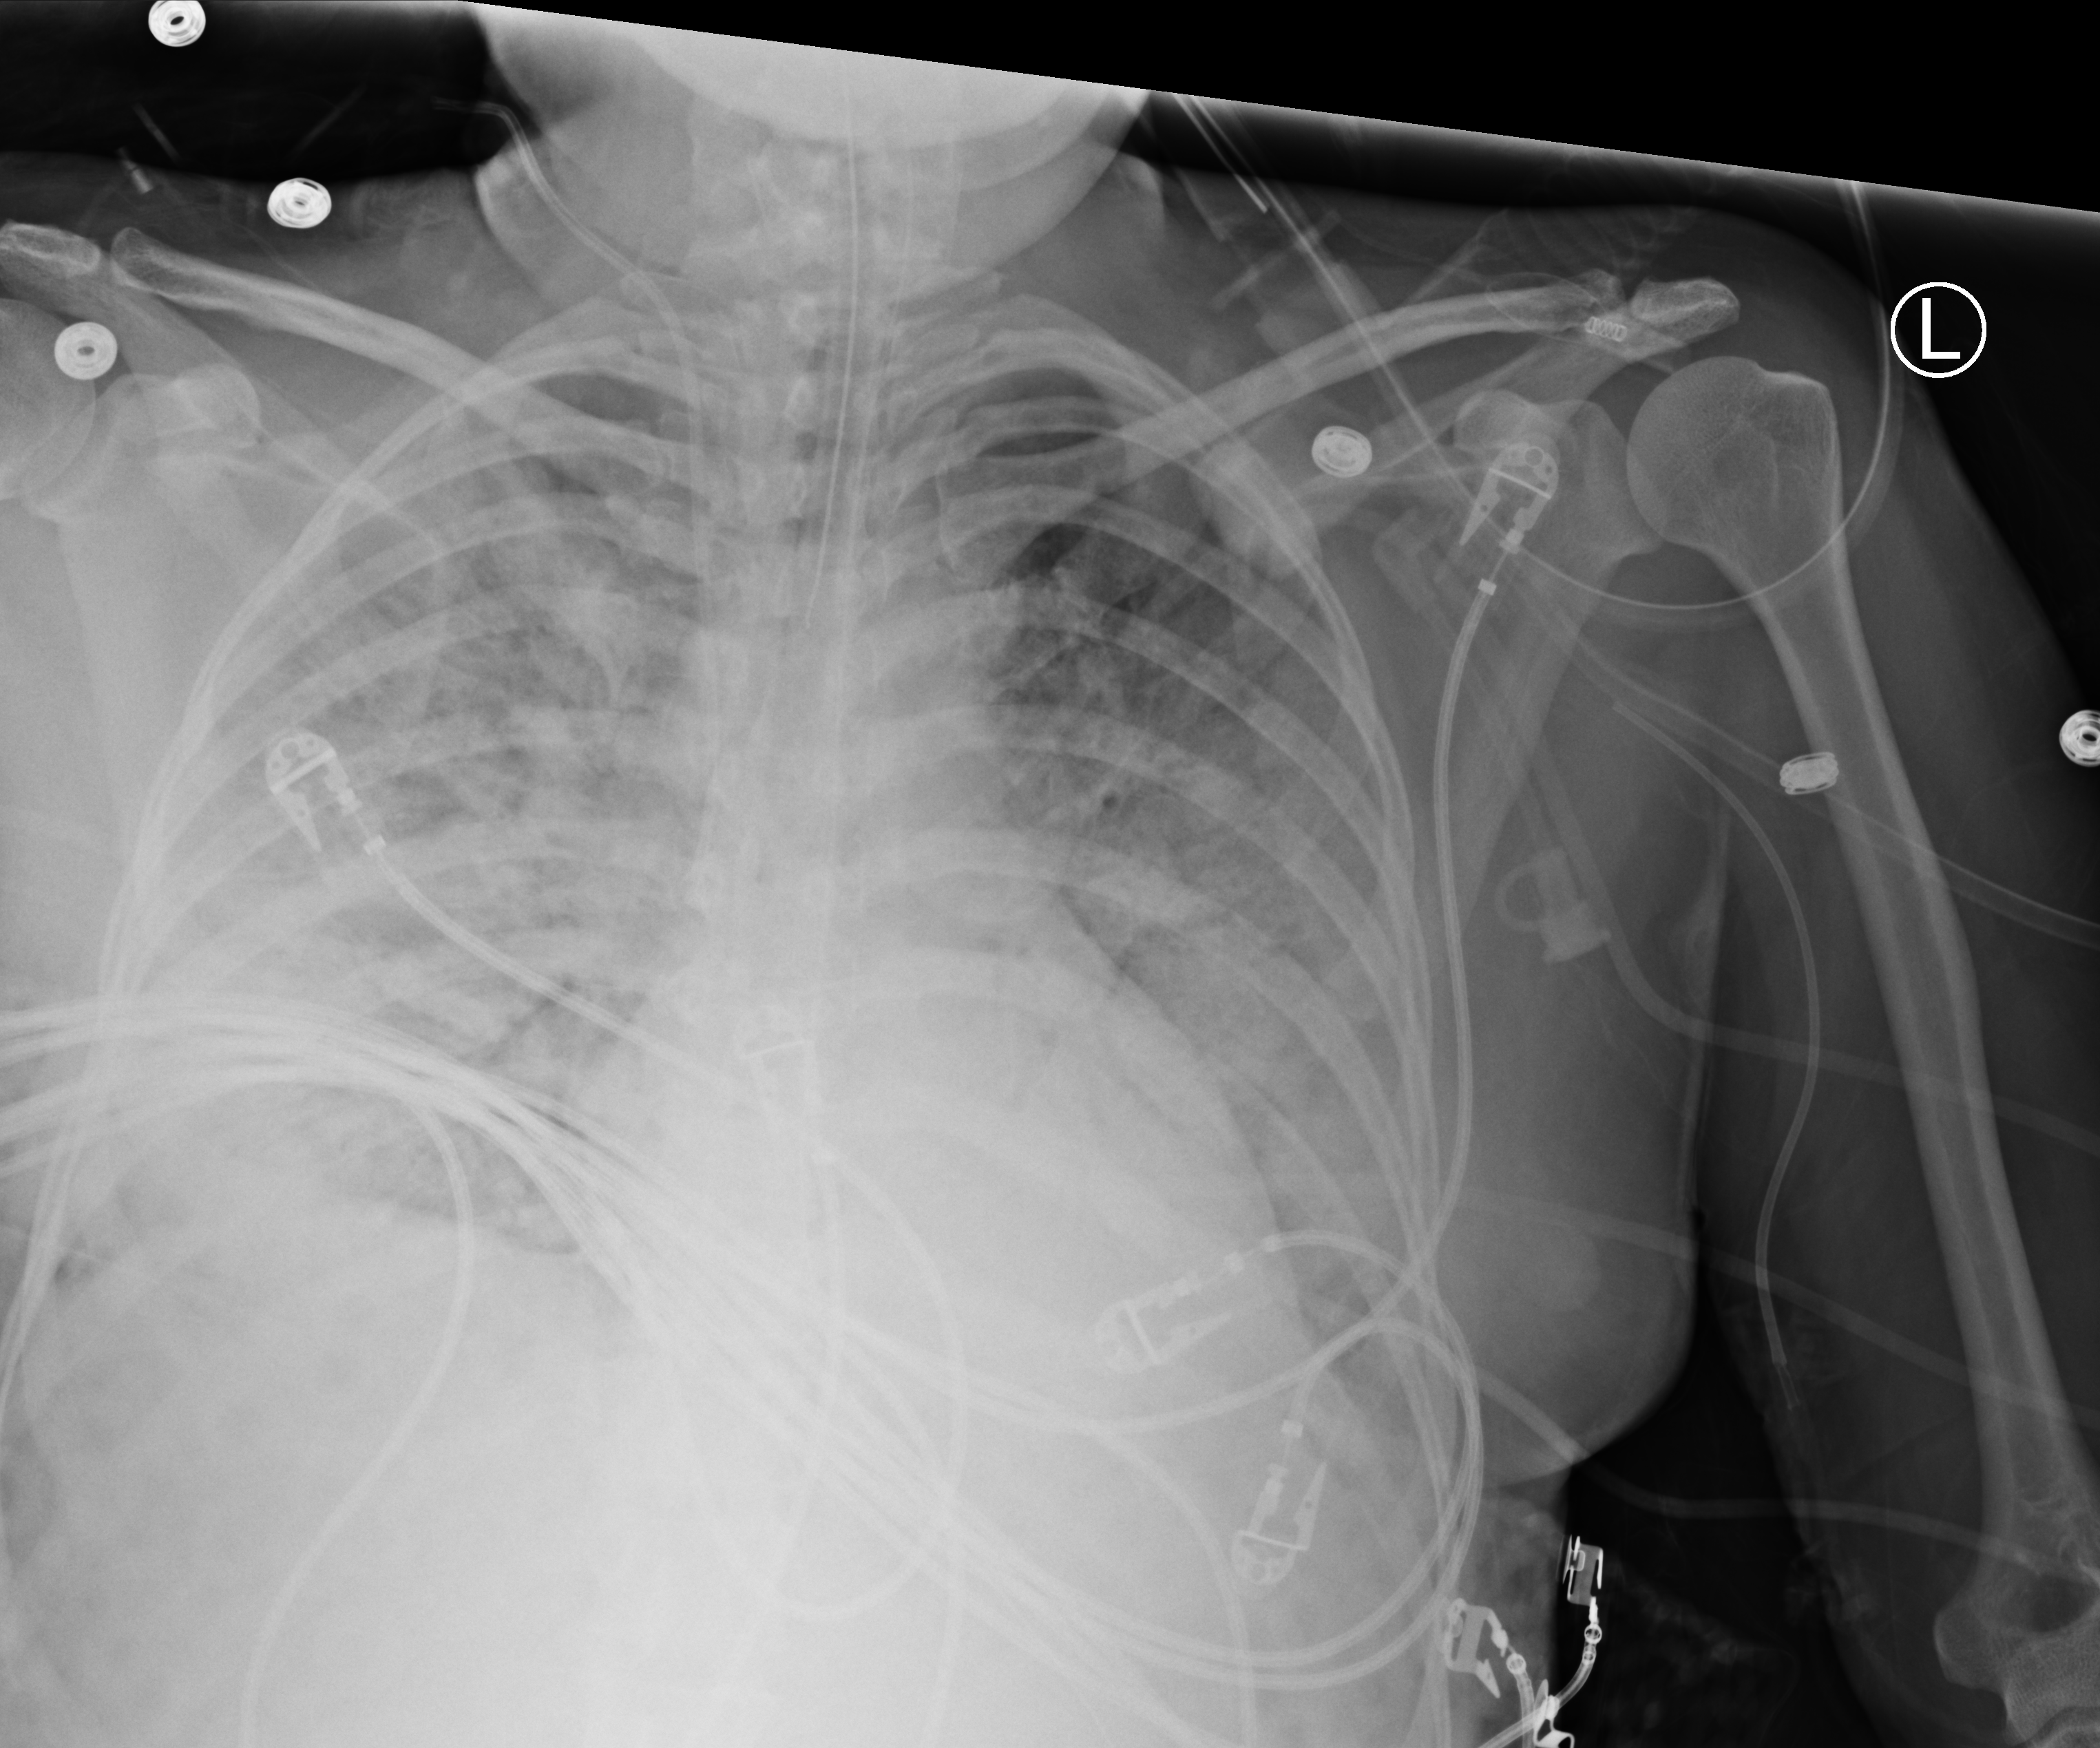
Chest X-ray (portable); anteroposterior (AP) projection. Patient hospitalised with COVID-19; female, aged 18–59 years.
Admission-level facts for this patient (not findings on this image; timing relative to this image not recorded):
- diabetes (admission record): no
- mechanically ventilated during this hospital stay: yes
- length of hospital stay: 71 days